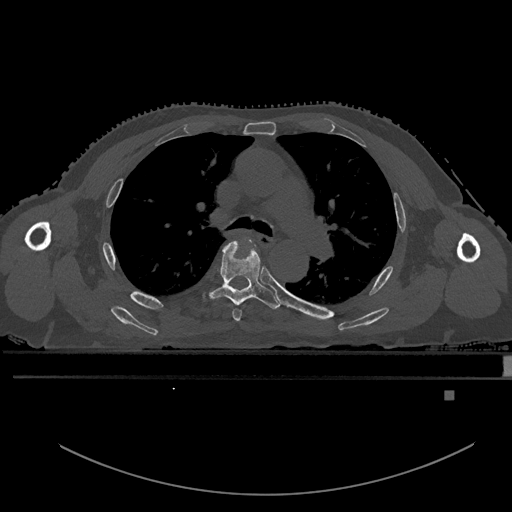
CT including the spine, one axial slice; slice 366 of 969 in the series (ordered by position); bone window (W 1800 / L 400 HU); 0.5 mm slice thickness; 512 × 512 image matrix, field of view 456 × 456 mm. Patient: male, 82 years. From the clinical record (not read from this slice): primary cancer: prostate; vertebrae with lytic lesions (as recorded): T11, T9, T8, T2.
Annotated regions visible in this slice (semi-automatically segmented with operator editing):
- T4 vertebra: bounding box (x1, y1, x2, y2) in pixels: (233, 238, 252, 322)
- T5 vertebra: (202, 240, 280, 310)